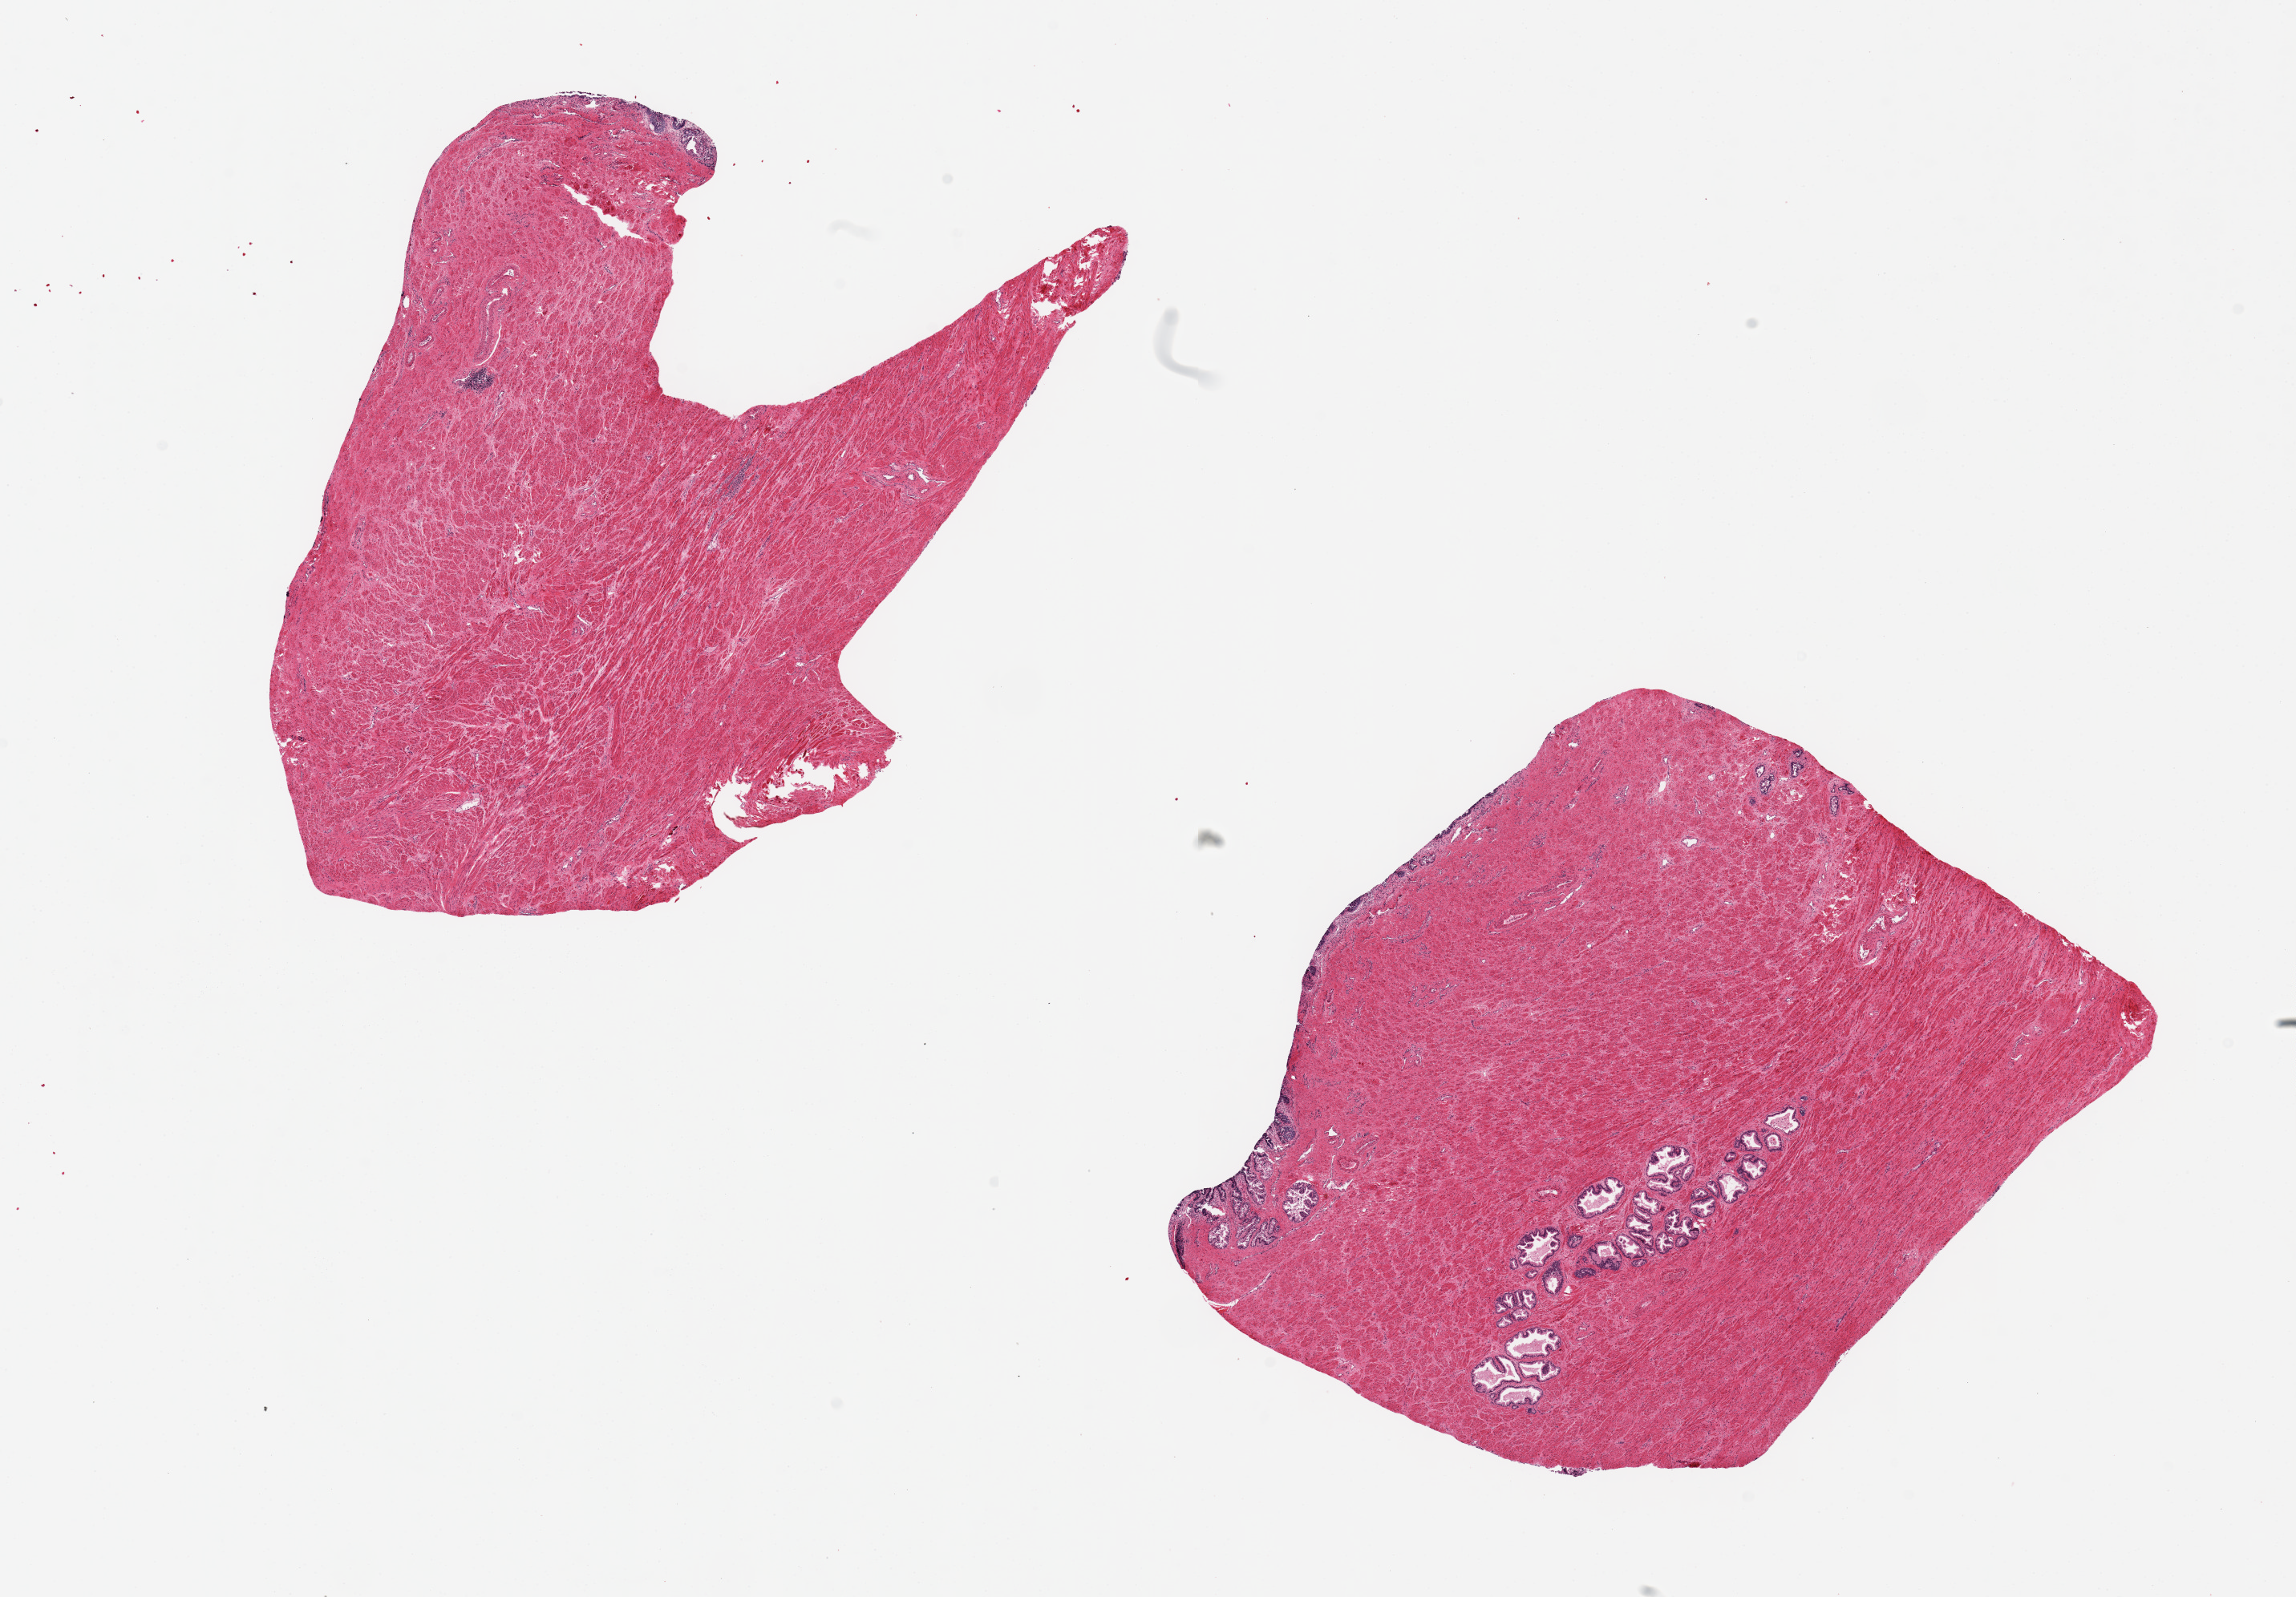
H&E whole-slide image, shown as a low-resolution overview of the whole scanned area (about 22.6 x 15.8 mm, slide scanned at 20x), PAXgene-fixed paraffin-embedded (PFPE) section, sampled site (target tissue): prostate, tissue donor sample. Donor sex: male.
Pathologist's review note for this sample: 2 pieces 8x6 & 7.5x6 mm; both contain prostatic urethra at one edge and are largely muscular; 1 has about 10% prostatic glands.